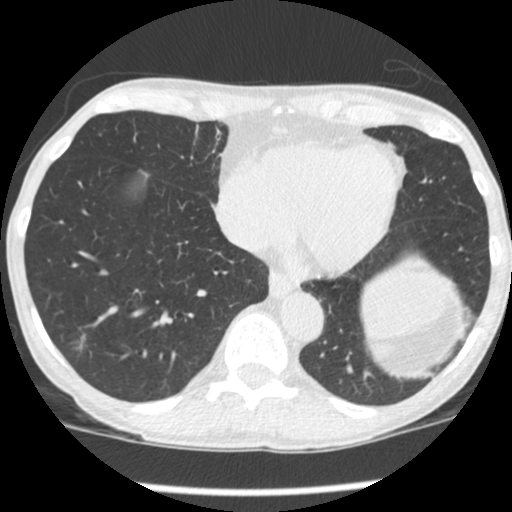
Low-dose screening chest CT, one axial slice. Position 82 of 248 along the scan axis. 120 kVp. Lung window (W 1500 / L -600 HU). 1.25 mm slice thickness. 512 × 512 image matrix, field of view 293 × 293 mm.
Outlined on this slice (outlined manually by an expert reader):
- lesion 1 (tumor, lower lobe of right lung): bounding box [x1, y1, x2, y2] px = [79, 336, 85, 349]